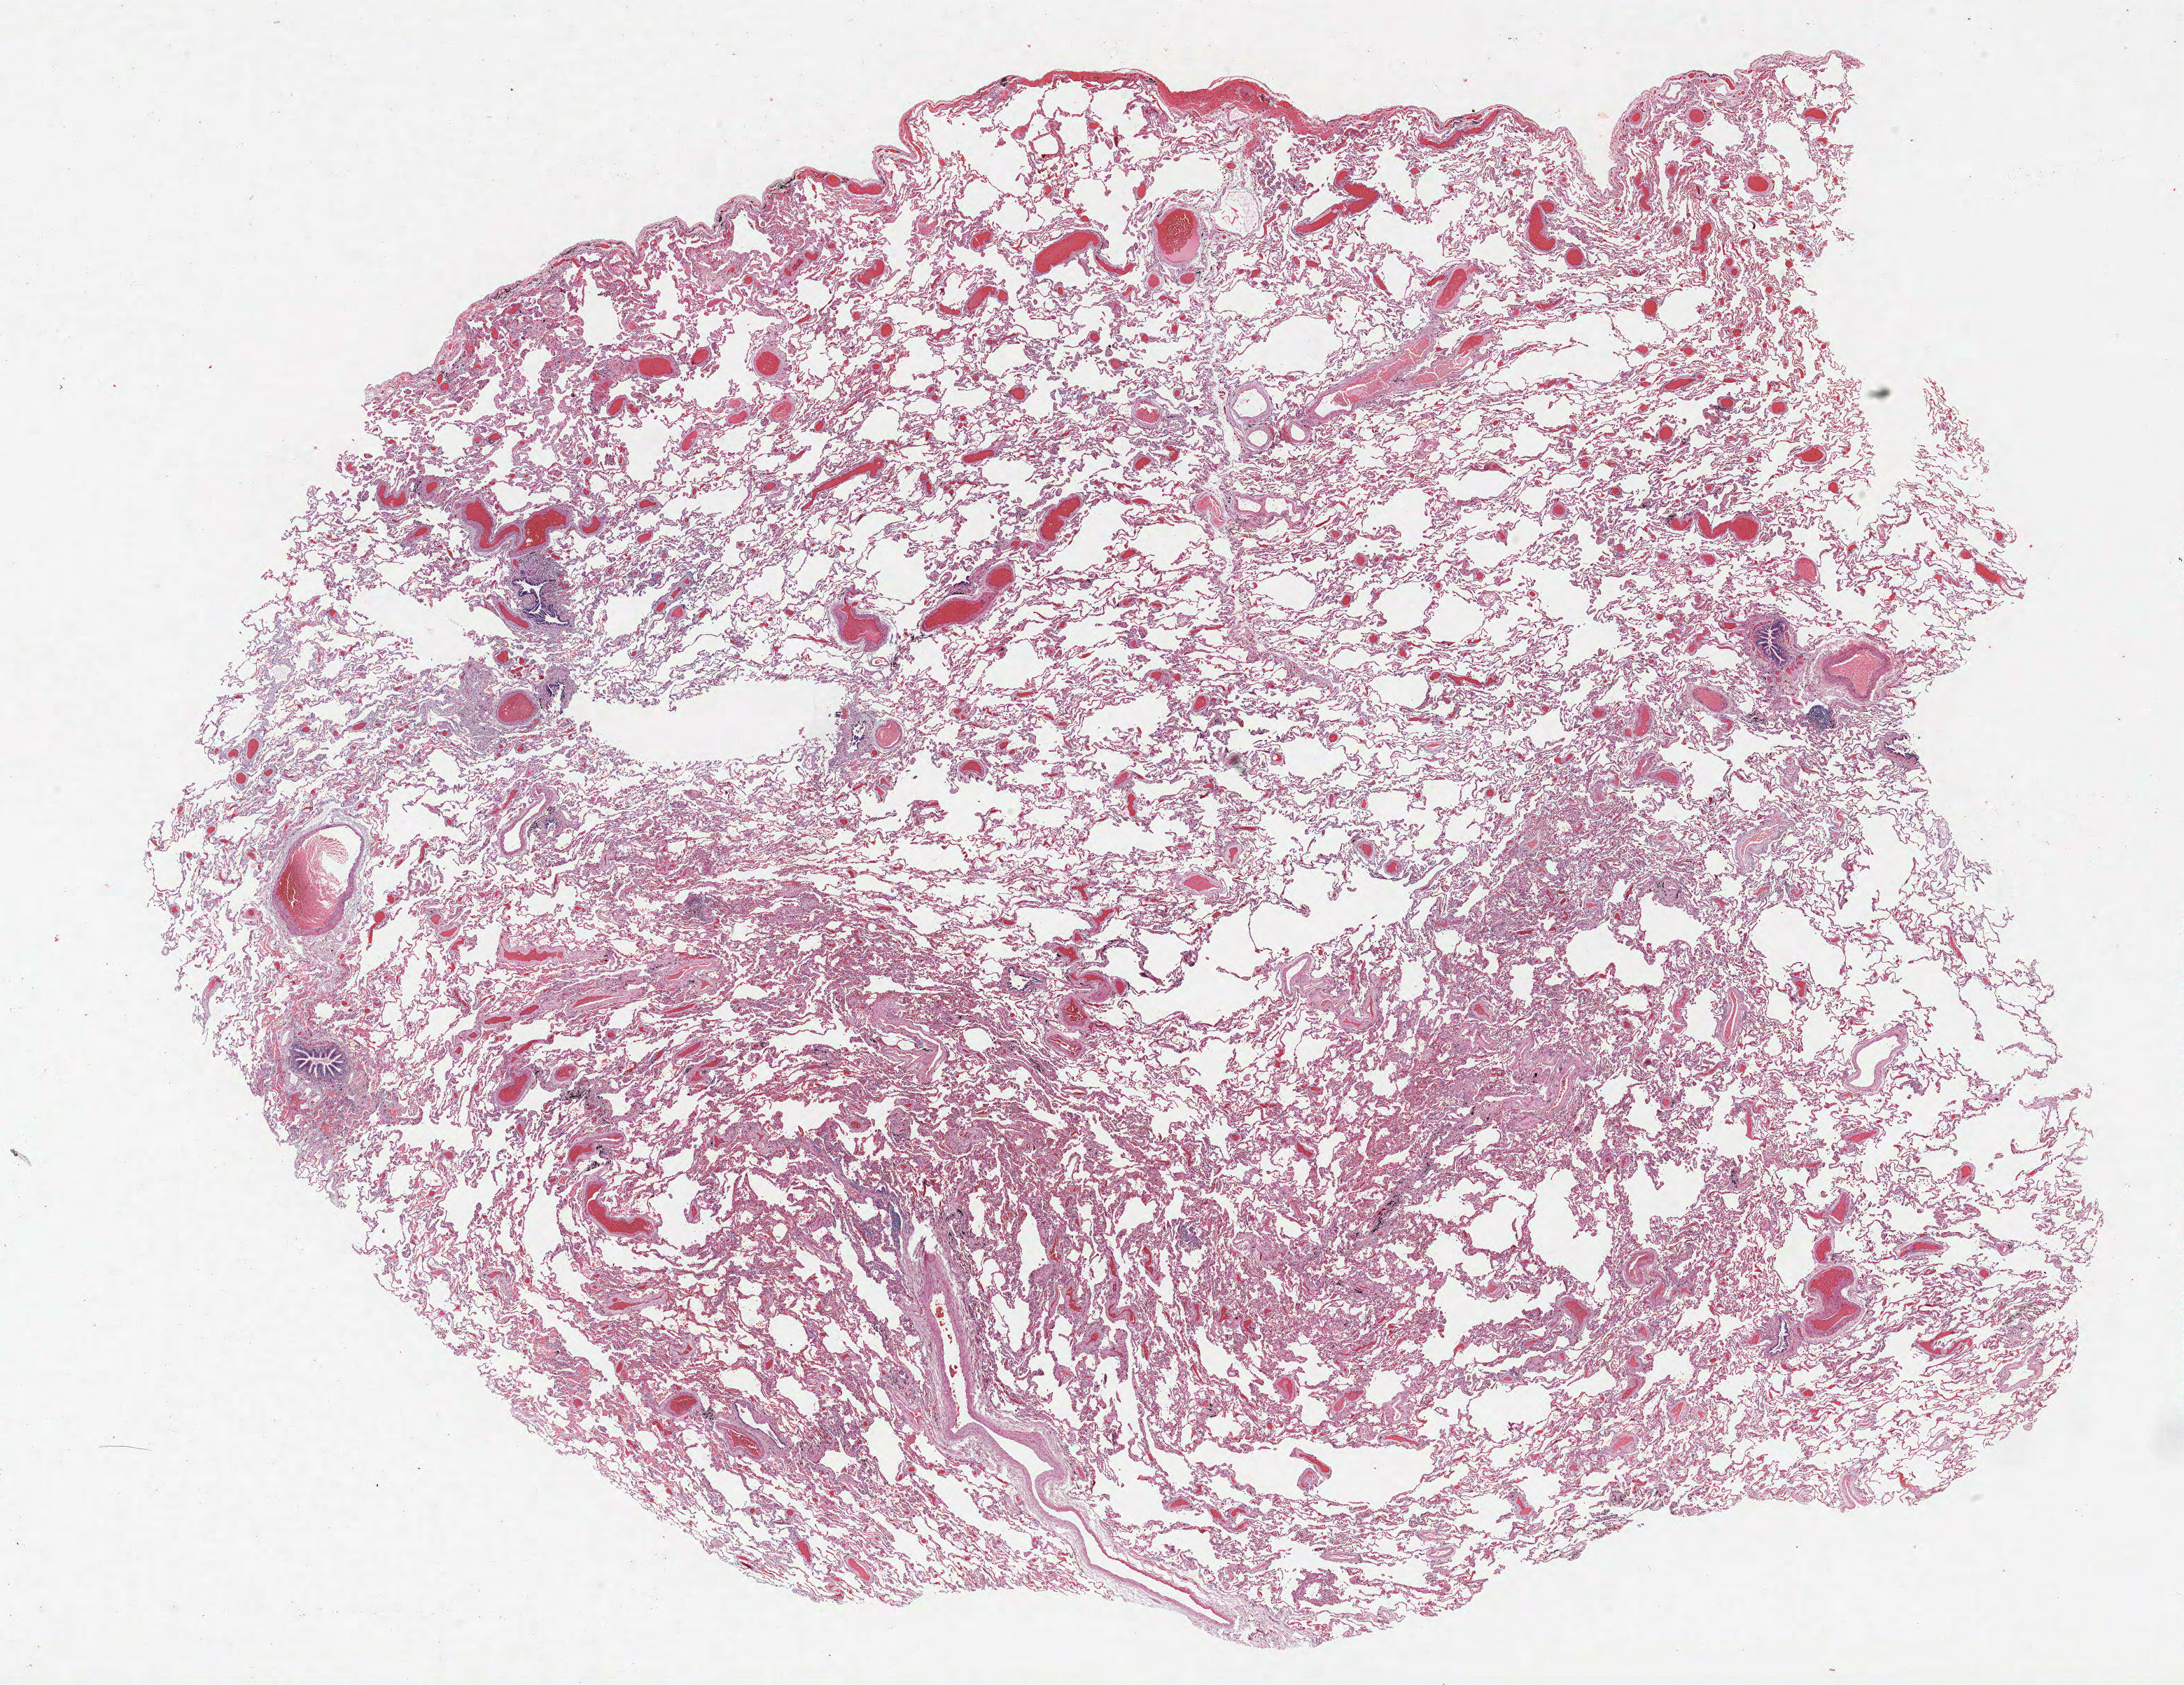
Hematoxylin and eosin (H&E) stained whole-slide image — shown as a low-resolution overview of the whole scanned area (about 25.0 x 19.3 mm). FFPE section. Lung tissue. Male patient, aged 73 at enrolment. Current smoker at enrolment. Grade: poorly differentiated (G3).
Tumour size (pathology): 22 mm. Stage (AJCC 6th edition): IA. ICD-O-3 topography: upper lobe of lung (C34.1). Primary tumour location (clinical record): right upper lobe. Participant's lung-cancer diagnosis: Adenocarcinoma, NOS.